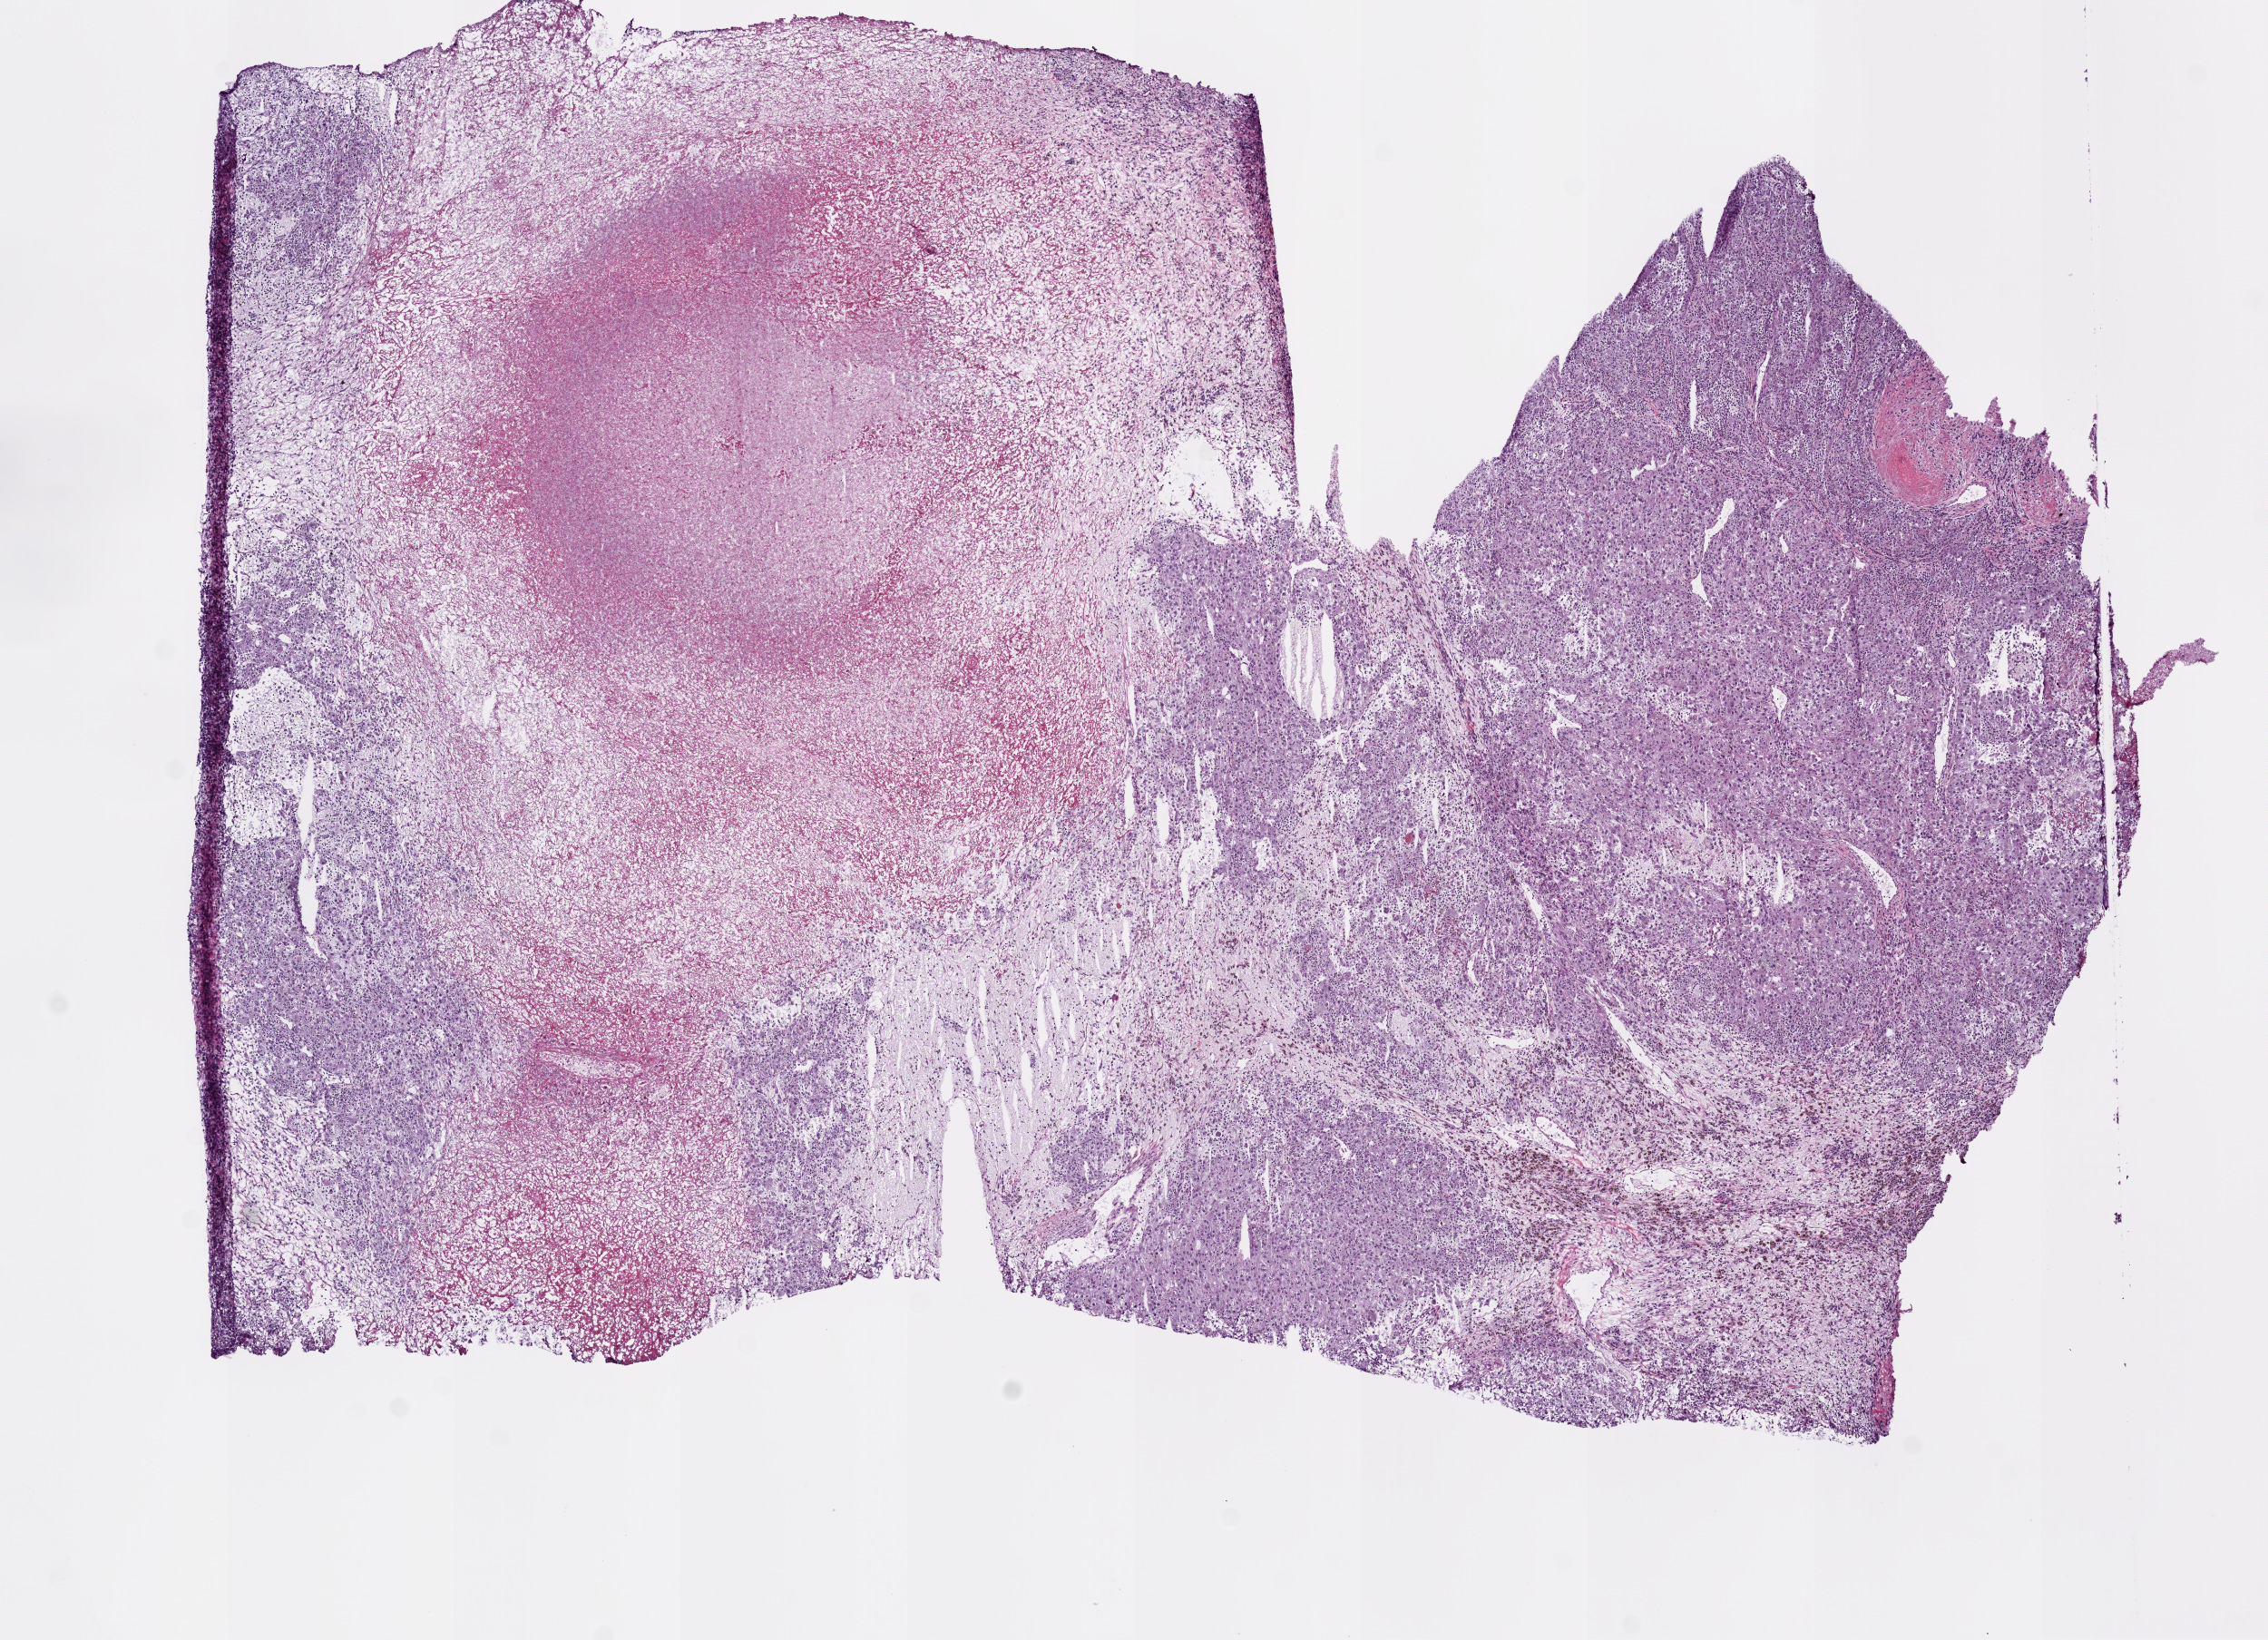
Whole-slide histology image, H&E-stained — a low-resolution overview of the entire scanned area, about 10.0 x 7.3 mm (acquisition: 20x scan), frozen section from the bottom of the tissue portion, primary tumour sample from the kidney. Patient: female, age at initial diagnosis 65 years. Histologic grade: G3 (poorly differentiated). Composition of this section per pathologist review: tumour cells 55%, tumour nuclei 80%, normal cells 0%, stromal cells 15%, necrosis 30%.
Diagnosis: Clear cell adenocarcinoma, NOS. AJCC pathologic stage: I (7th edition).